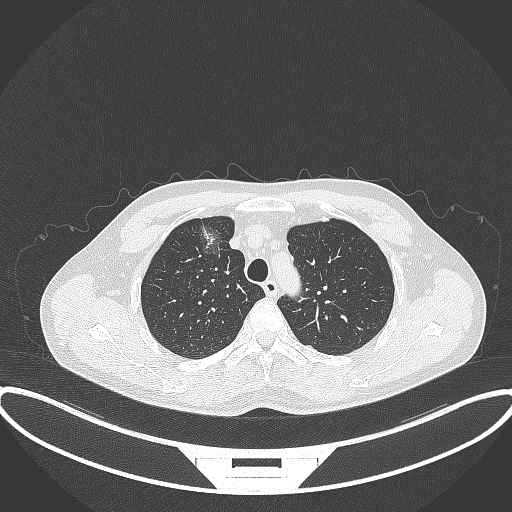
Chest CT, one axial slice; position 289 of 395 along the scan axis; reconstruction kernel B70f; 120 kVp; lung window (W 1500 / L -600 HU); 512 × 512 image matrix. Patient: male, 60 years. Case-level facts recorded for this patient, not image findings: clinical TNM (as recorded): T1c N0 M0.
Annotated regions visible in this slice (rectangle marked by the reading radiologist):
- lung tumour (recorded histology: adenocarcinoma): box from (x=188, y=211) to (x=229, y=266) px